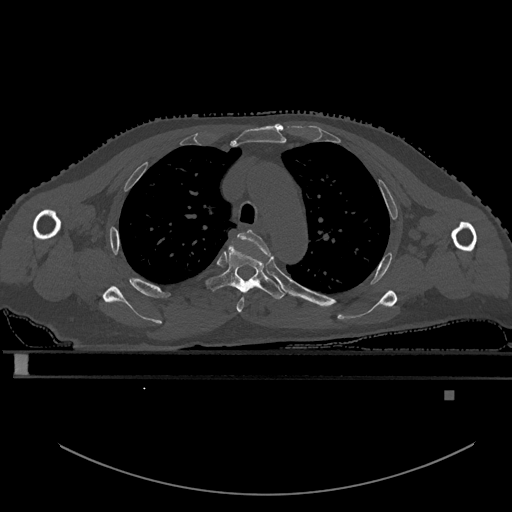
CT including the spine, one axial slice; position 418 of 969 along the scan axis; bone window (W 1800 / L 400 HU); 512 × 512 image matrix. Male patient, age 82 years. From the clinical record (not read from this slice): primary cancer: prostate; vertebrae with lytic lesions (as recorded): T11, T9, T8, T2.
Structures marked on this image (semi-automatically segmented with operator editing):
- T3 vertebra: bounding box <236,230,271,313> (left, top, right, bottom; pixels)
- T4 vertebra: <206,245,285,299>